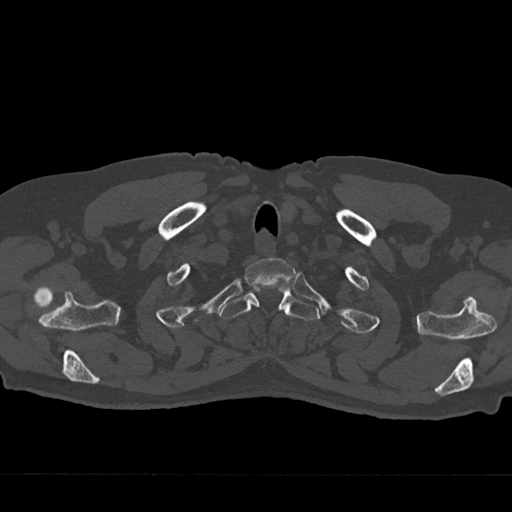
CT including the spine, one axial slice; position 630 of 797 along the scan axis; reconstruction kernel Br40s/3; 120 kVp; bone window (W 1800 / L 400 HU); 0.5 mm slice thickness; 512 × 512 image matrix. Patient: male, 75 years. From the clinical record (not read from this slice): primary cancer: renal.
Outlined on this slice (semi-automatically segmented with operator editing):
- T1 vertebra: bounding box [x1, y1, x2, y2] px = [244, 258, 294, 287]
- T2 vertebra: [220, 289, 319, 321]